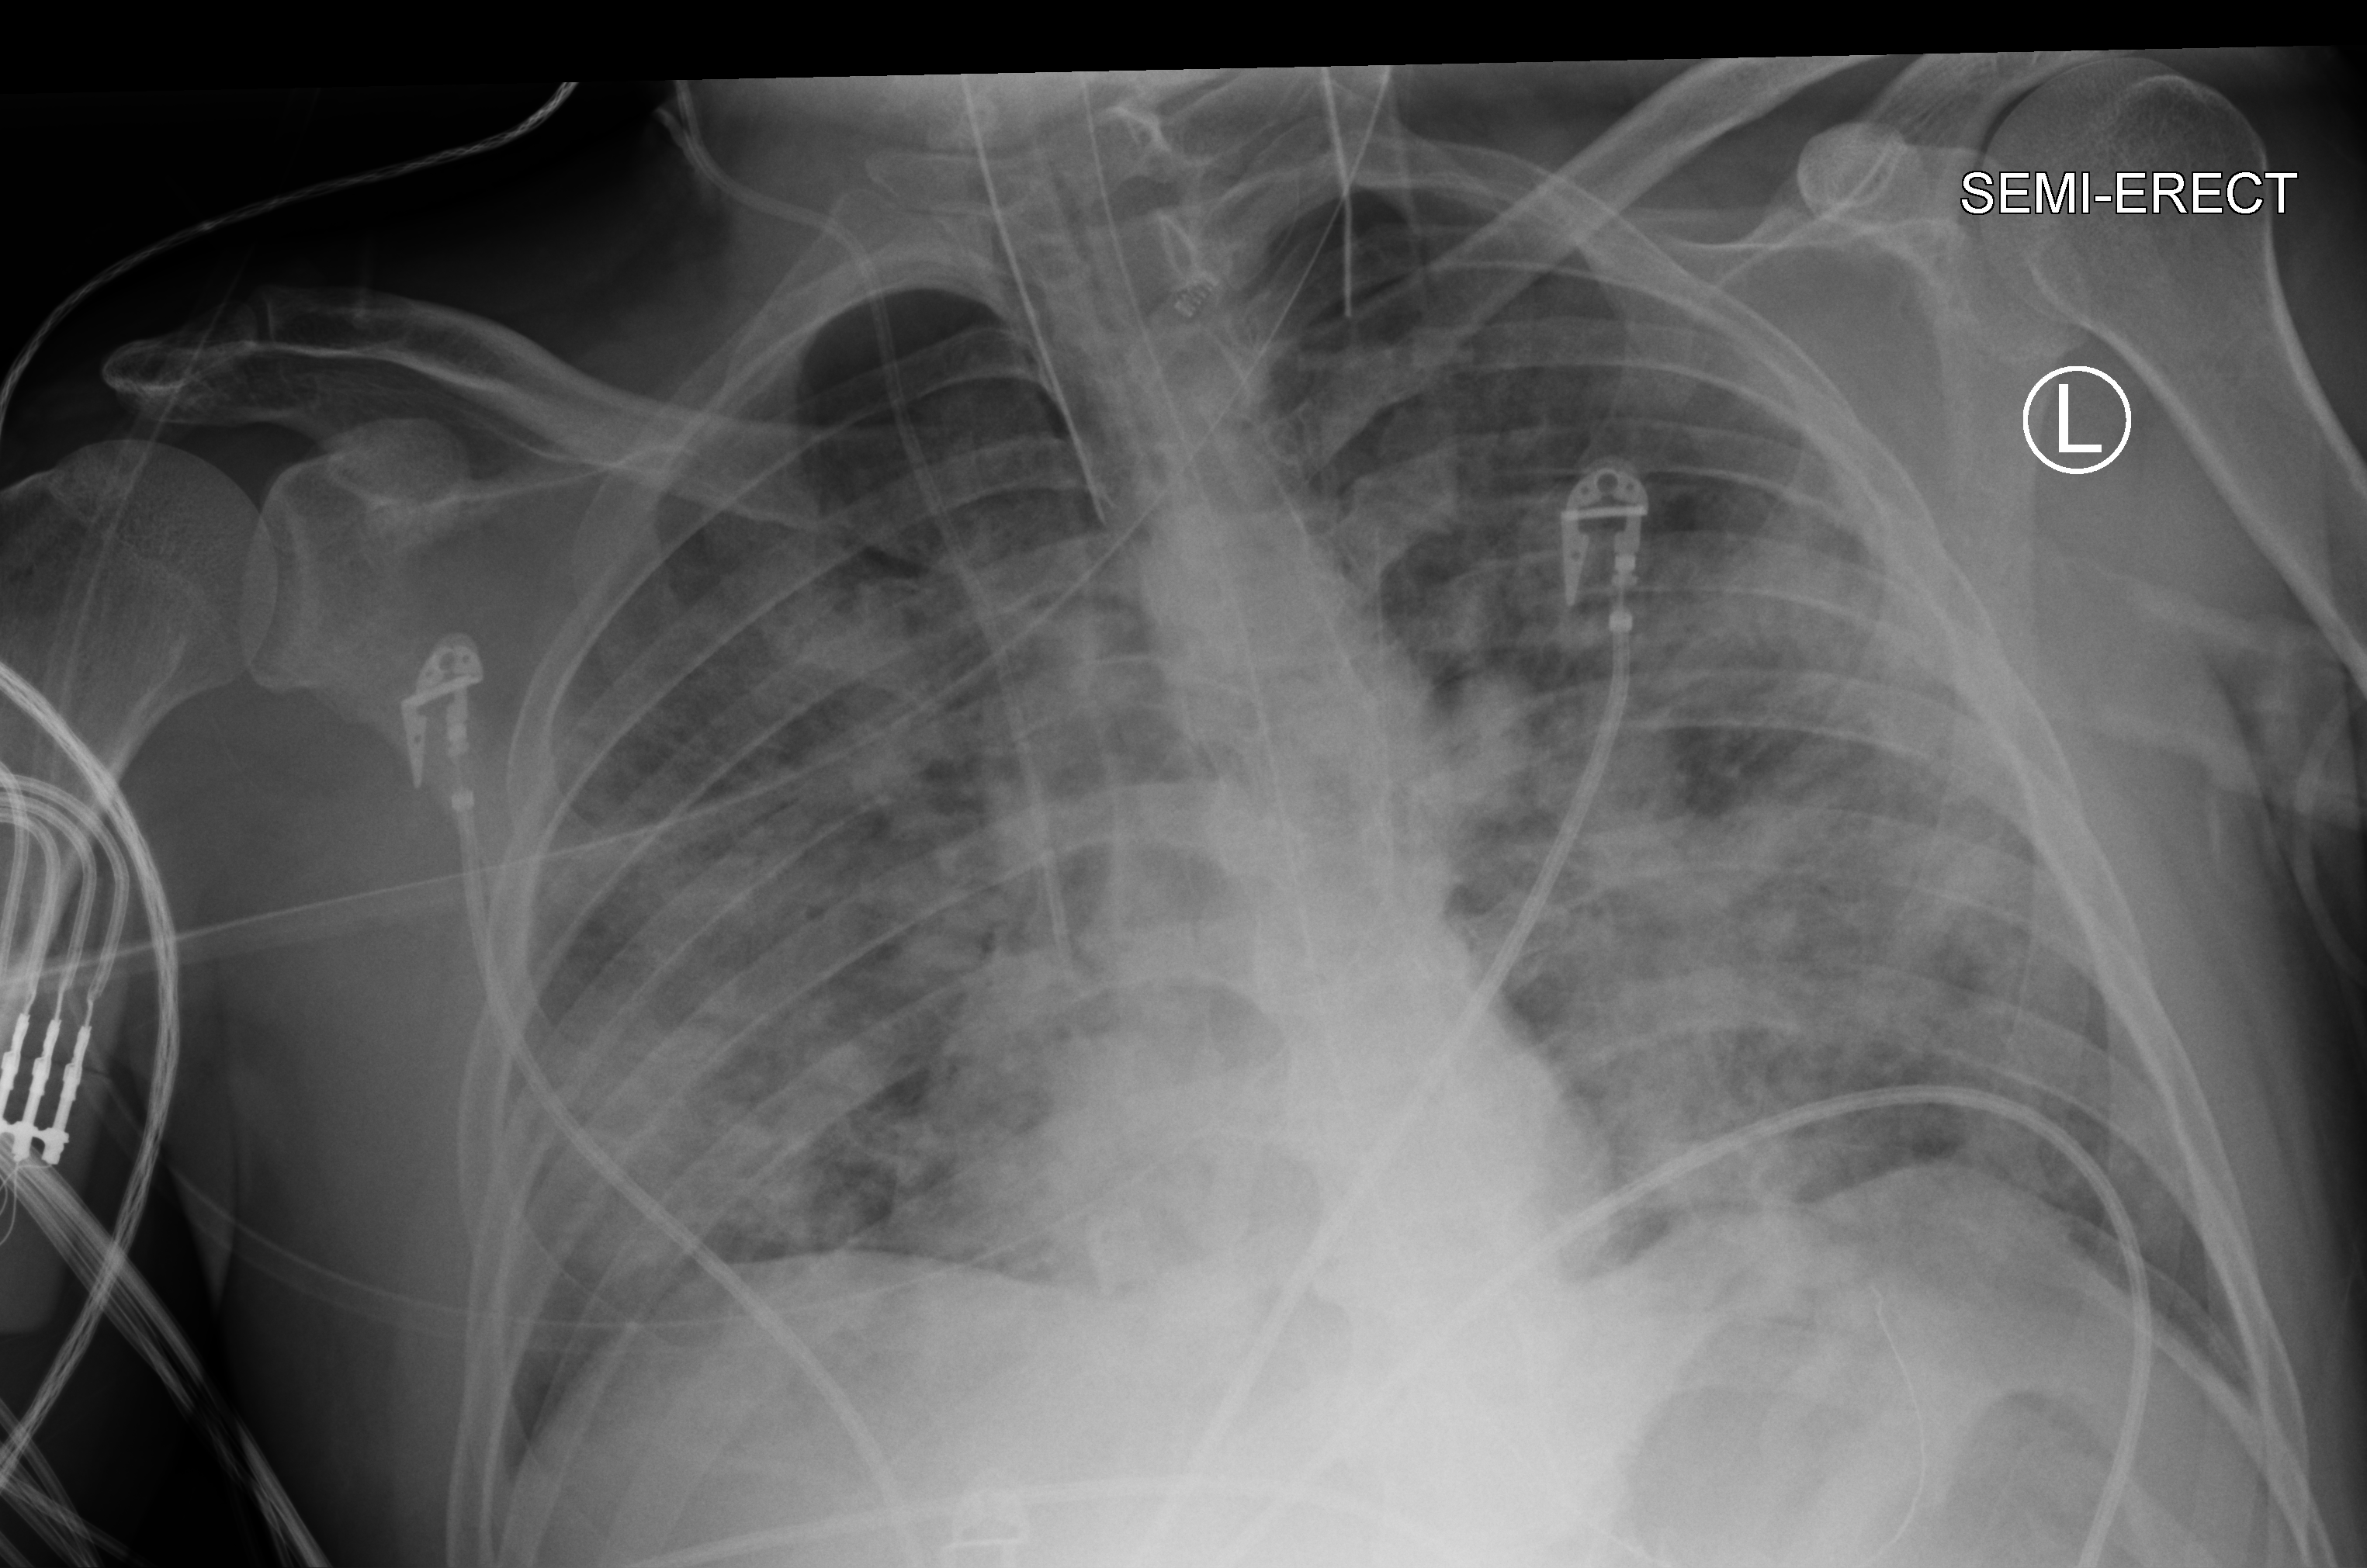
Bedside chest radiograph (computed radiography); anteroposterior (AP) projection. Patient hospitalised with COVID-19; male, aged 18–59 years.
From the hospital-stay record, not from the radiograph (when in the stay this image was taken is not recorded): length of hospital stay: 29 days; mechanically ventilated during this hospital stay: yes; admitted to intensive care during this hospital stay: yes.